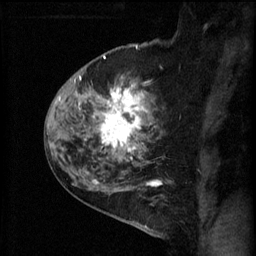
Breast MRI (dynamic contrast-enhanced), one sagittal slice. Slice 42 of 60 in the series (ordered by position). 3 images stored at this slice position (order not interpretable as contrast timing). 1.5 T. TE 4.2 ms, TR 11 ms. 256 × 256 image matrix, field of view 180 × 180 mm. Female patient, age 52 years.
Outlined on this slice (semi-automatic segmentation, software-assisted and operator-edited):
- analysis volume of interest (the breast-tissue region the enhancement analysis was run in; not a lesion): bounding box <86,76,165,157> (left, top, right, bottom; pixels)
- tumour enhancement mask (voxels above the 70 % enhancement threshold inside the analysis volume of interest): <91,82,147,157>